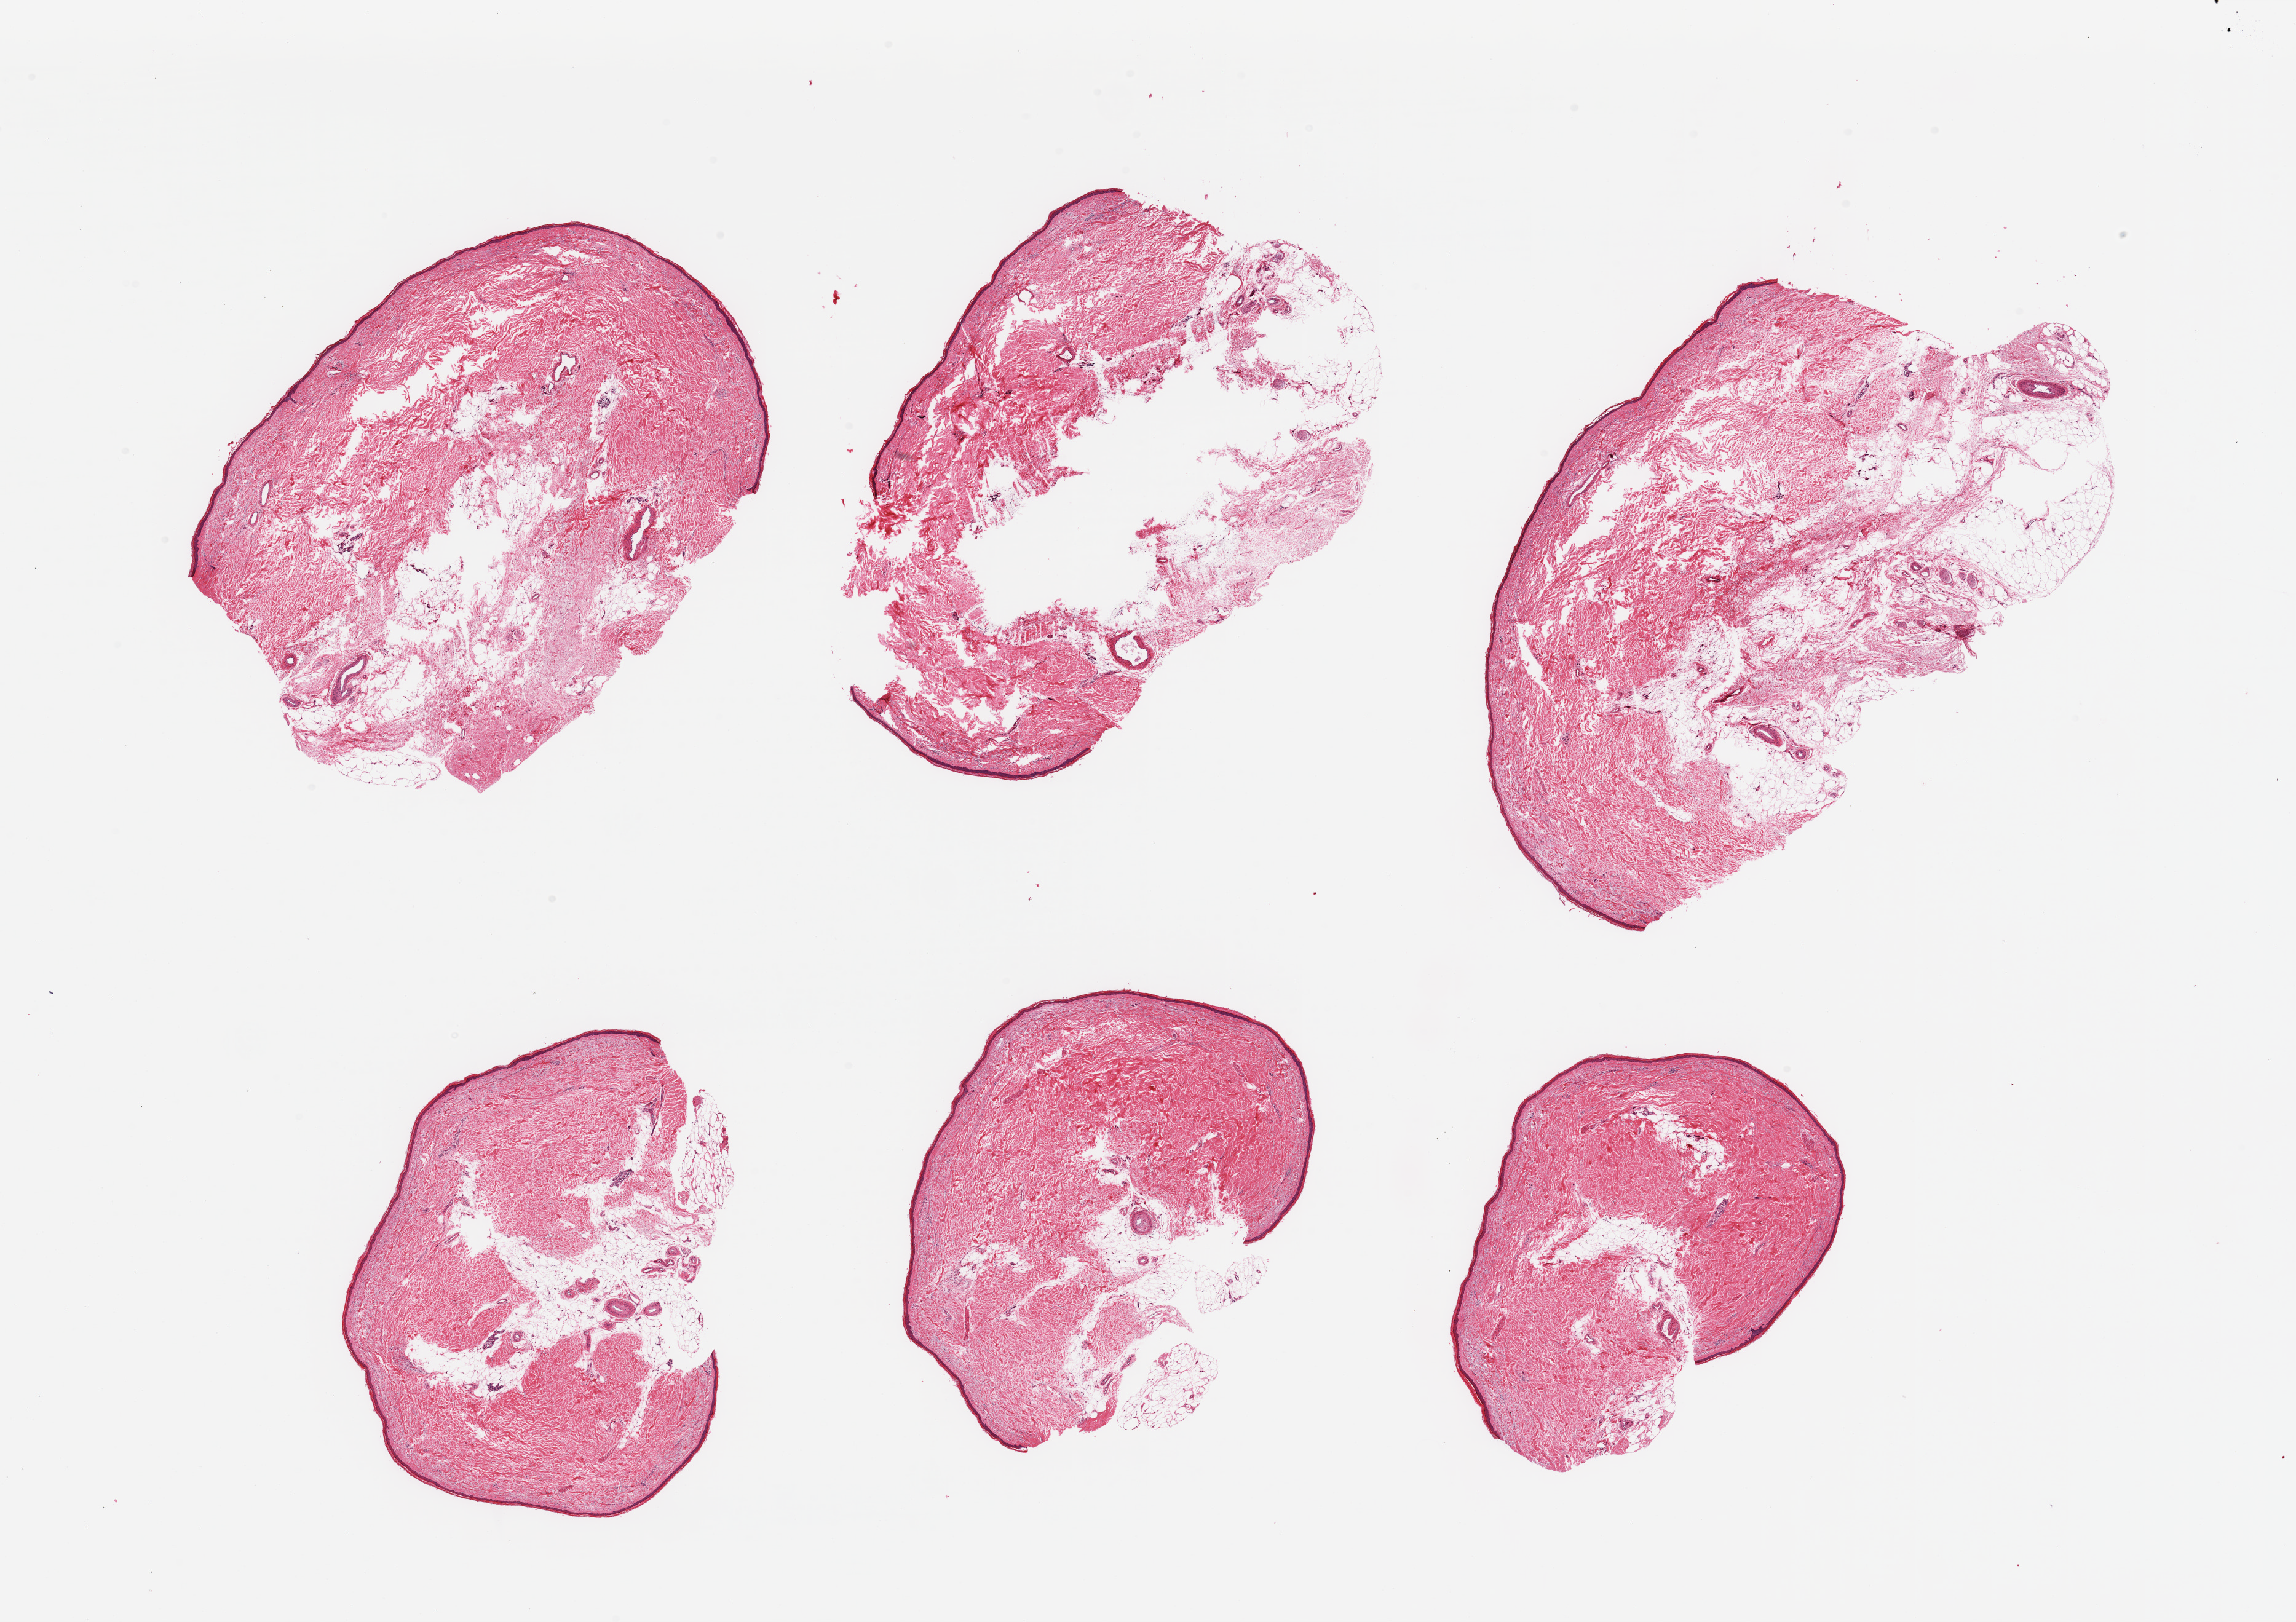
H&E whole-slide image, brightfield — shown as a low-resolution overview of the whole scanned area (about 29.5 x 20.9 mm). PAXgene-fixed paraffin-embedded (PFPE) section. Target tissue: skin of lower leg. Donor tissue sample. Donor sex: female.
* pathologist's review note for this sample: 6 pieces; from 10% to 50% internal/external fat; epidermis 35microns thick